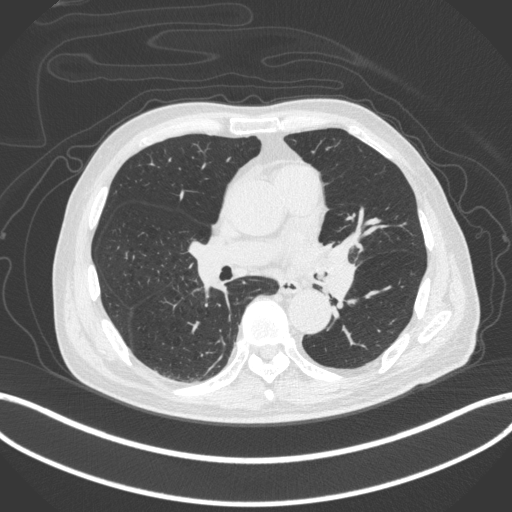
Chest CT, one axial slice. Reconstruction kernel B31f. 120 kVp. Lung window (W 1500 / L -600 HU). 1 mm slice thickness. 512 × 512 image matrix, field of view 400 × 400 mm. Male patient, age 77 years. Case-level facts recorded for this patient, not image findings: clinical TNM (as recorded): T3 N1 M0.
Annotated regions visible in this slice (rectangle marked by the reading radiologist):
- lung tumour (recorded histology: adenocarcinoma): bounding box <316,236,357,296> (left, top, right, bottom; pixels)